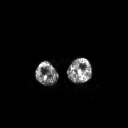
FDG PET of an extremity soft-tissue mass (from a PET/CT study), one axial slice. Position 198 of 267 along the scan axis. 3.27 mm slice thickness. 128 × 128 image matrix. Patient: male, 44 years. Case-level facts recorded for this patient, not image findings: histological type: undifferentiated pleomorphic liposarcoma; grade: high; site of the primary tumour: left thigh.
Structures marked on this image (expert contour drawn on MRI and transferred to this co-registered scan by the dataset authors):
- gross tumour volume including surrounding oedema: bounding box [x1, y1, x2, y2] px = [71, 69, 86, 76]